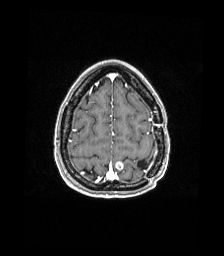
Brain MRI from a brain-tumour surgery series, one axial slice; position 41 of 176 along the scan axis; T1-weighted post-contrast; 1 mm slice thickness; 224 × 256 image matrix. From the clinical record (not read from this slice): histopathology: Atypical meningioma; WHO grade: 2; tumour location: Paramedian Left Parietal.
Annotated regions visible in this slice (manually delineated by an expert):
- previous resection cavity: bounding box [x1, y1, x2, y2] px = [137, 160, 147, 169]
- tumour: [115, 161, 124, 170]